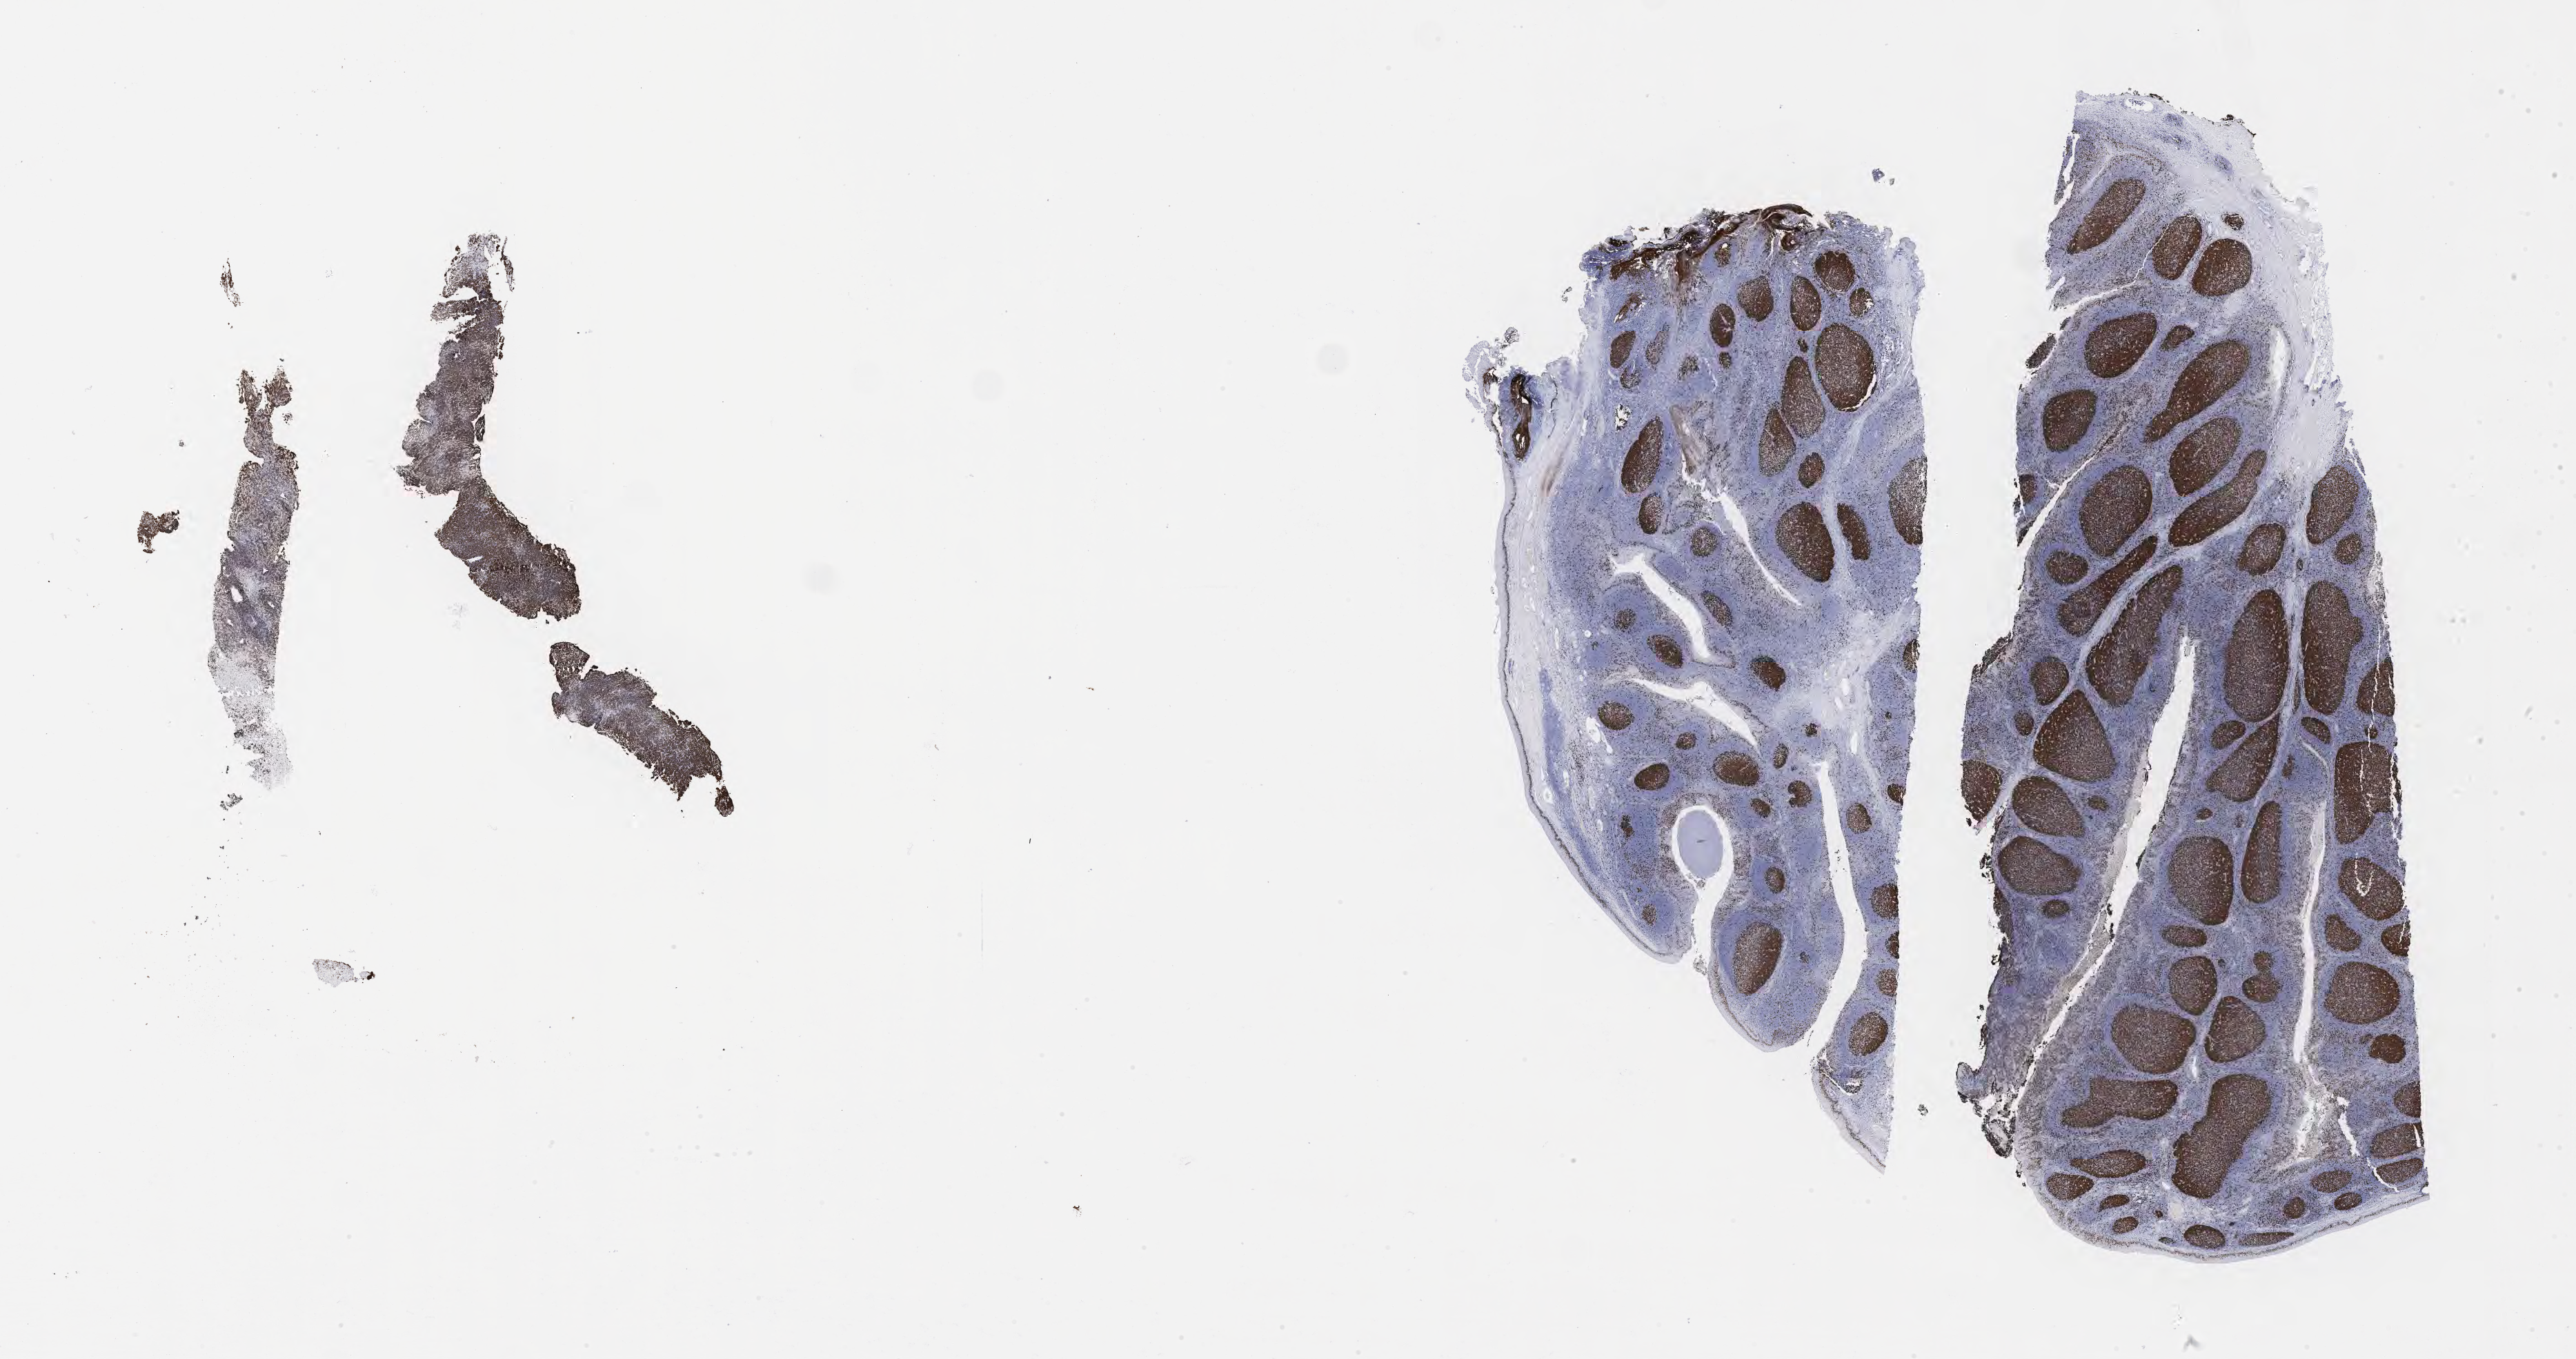
Whole-slide image, immunohistochemical stain for Ki-67 — whole scanned area (about 30.2 x 15.9 mm) shown as a low-resolution overview. Specimen: tumor tissue. Female patient, aged 12.
Histologic diagnosis: Burkitt lymphoma, NOS.